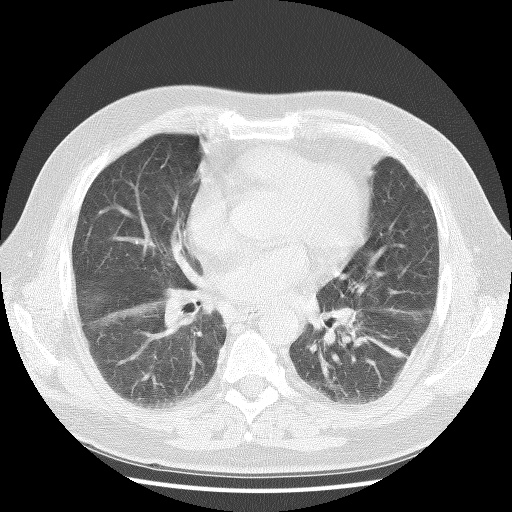
Chest CT (low-dose screening protocol), one axial image, baseline annual screen, lung window (W 1500 / L -600 HU), 2.5 mm slice thickness, lung (sharp) reconstruction kernel (BONE), slice 53 of 111 in the series. Male participant, aged 59 years at enrolment.
Expert reader's lesion annotation, bounding box [x1, y1, x2, y2] px = [307, 287, 381, 358]. The exam's reader record, not a measurement of the box and not confirmed to be the same lesion: non-calcified nodule or mass ≥4 mm, right upper lobe, 4 × 4 mm, soft tissue attenuation. Note: the box lies in the patient's left hemithorax on this image, whereas the reader's record names the right lung; they may be different findings.